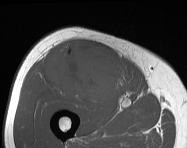
MRI of an extremity soft-tissue mass, one axial slice; MR volume resampled by the dataset authors to the PET/CT grid (not the native acquisition matrix); 3.27 mm slice thickness; 187 × 148 image matrix, field of view 183 × 145 mm. Male patient. Case-level facts recorded for this patient, not image findings: histological type: pleiomorphic leiomyosarcoma; grade: intermediate; site of the primary tumour: right thigh.
Structures marked on this image (expert contour drawn on MRI and transferred to this co-registered scan by the dataset authors):
- gross tumour volume including surrounding oedema: bounding box (x1, y1, x2, y2) in pixels: (45, 40, 128, 101)
- gross tumour volume (mass): (45, 40, 128, 101)